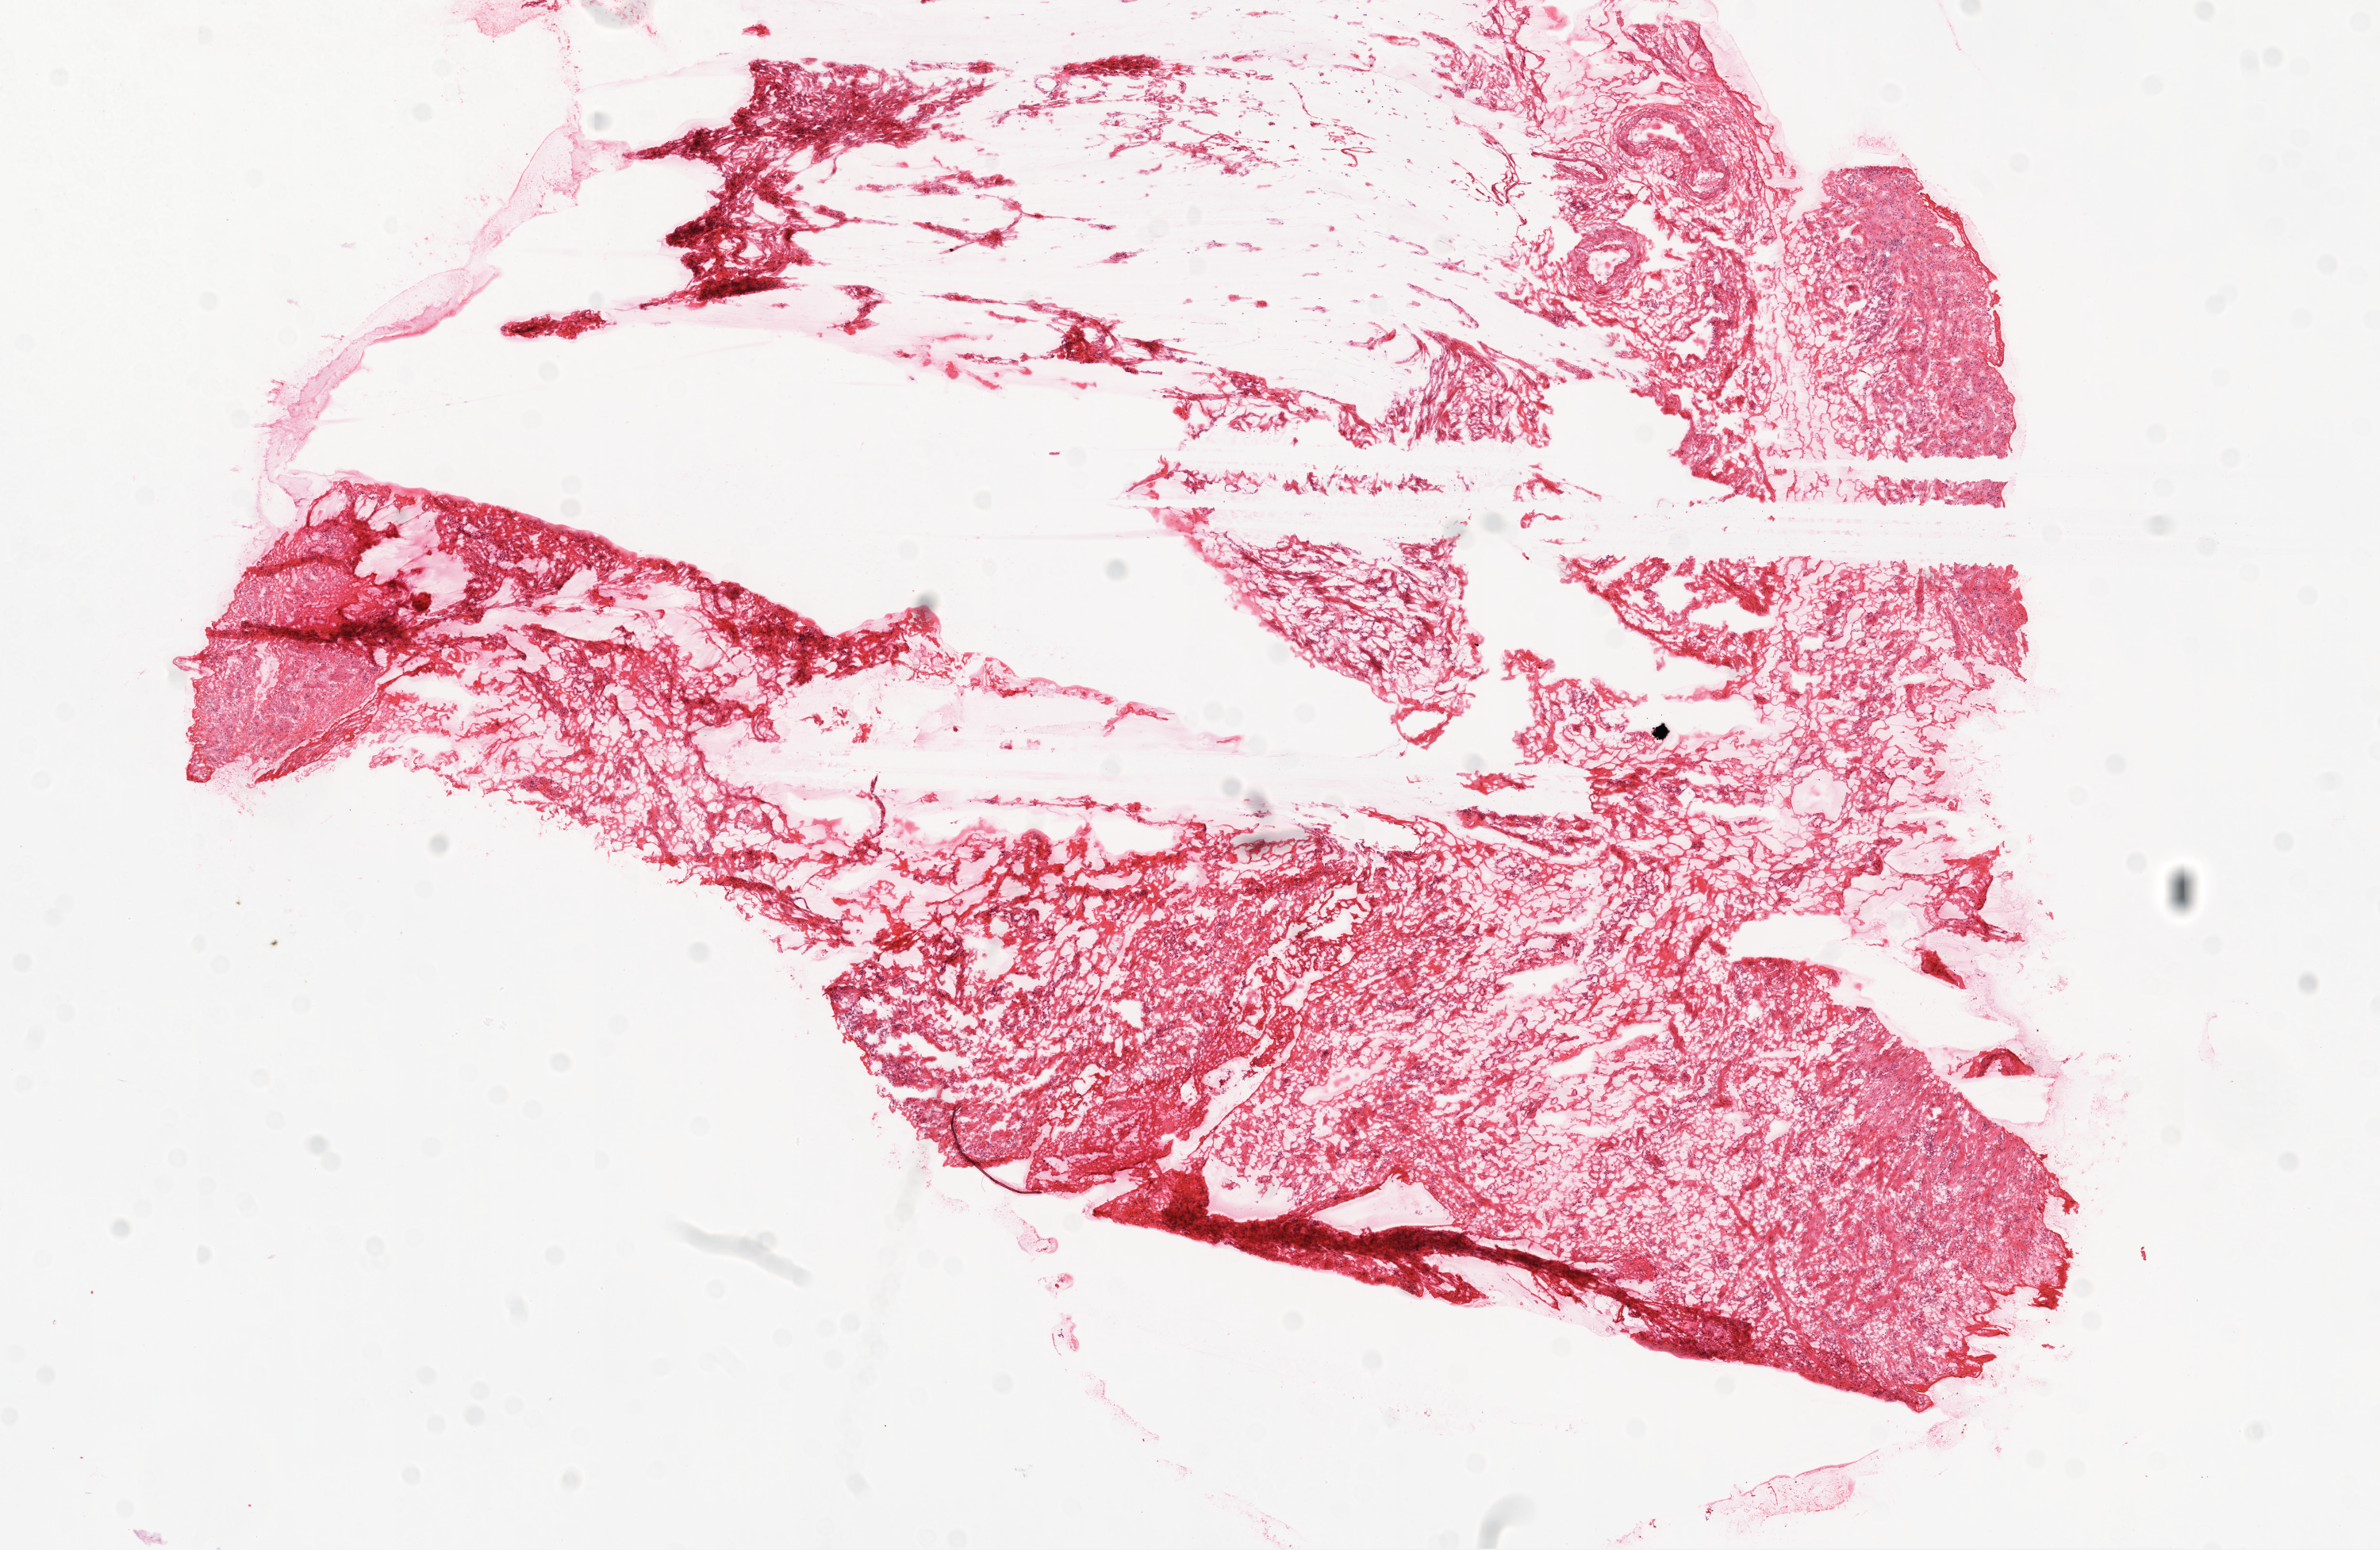
Hematoxylin and eosin (H&E) stained whole-slide image, whole scanned area (about 12.0 x 7.8 mm, slide scanned at 20x) shown as a low-resolution overview, frozen section, ovary, solid tissue normal (non-tumour tissue) sample. Patient: female, age at initial diagnosis 53 years.
* this section: solid tissue normal sample (biorepository sample class)
* patient diagnosis: Serous cystadenocarcinoma, NOS